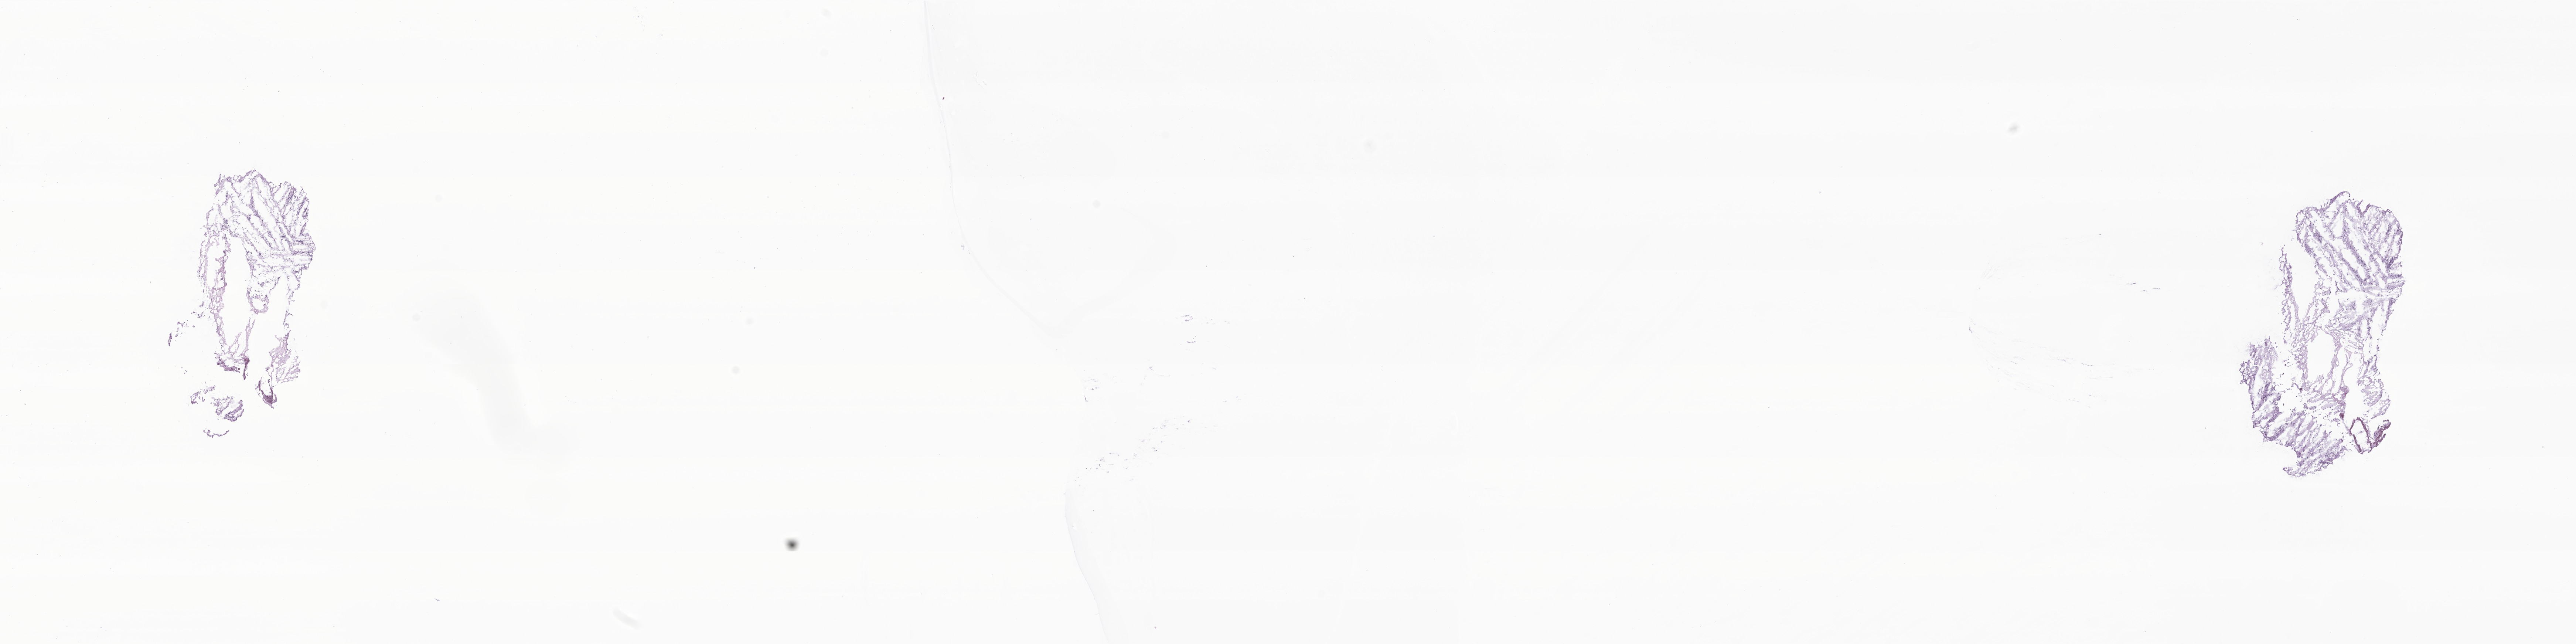
Whole-slide image, haematoxylin and eosin stain of tumor tissue from the brain — shown as a low-resolution overview of the whole scanned area (about 29.3 x 7.3 mm), frozen section. Patient: female, age 460 days (about 1.3 years).
Diagnosis (ICD-O-3 morphology term): Neoplasm, uncertain whether benign or malignant.